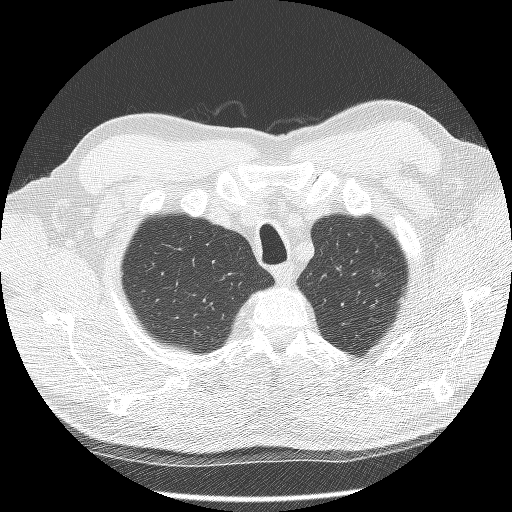
Axial slice from a low-dose chest CT screening exam, second screening round (one year after baseline), lung window (W 1500 / L -600 HU), 2.5 mm slice thickness, lung (sharp) reconstruction kernel (BONE). Male participant, aged 60 years at enrolment. Former smoker at enrolment.
- Lesion marked by an expert reader, bounding box (x1, y1, x2, y2) in pixels: (343, 257, 399, 301).
- The screening reader recorded 2 non-calcified nodules or masses ≥4 mm on this exam (right lower lobe, left upper lobe); which of them this box marks is not recorded.
- Official screen result: positive, no significant change: stable abnormalities potentially related to lung cancer, unchanged since the prior screening exam.